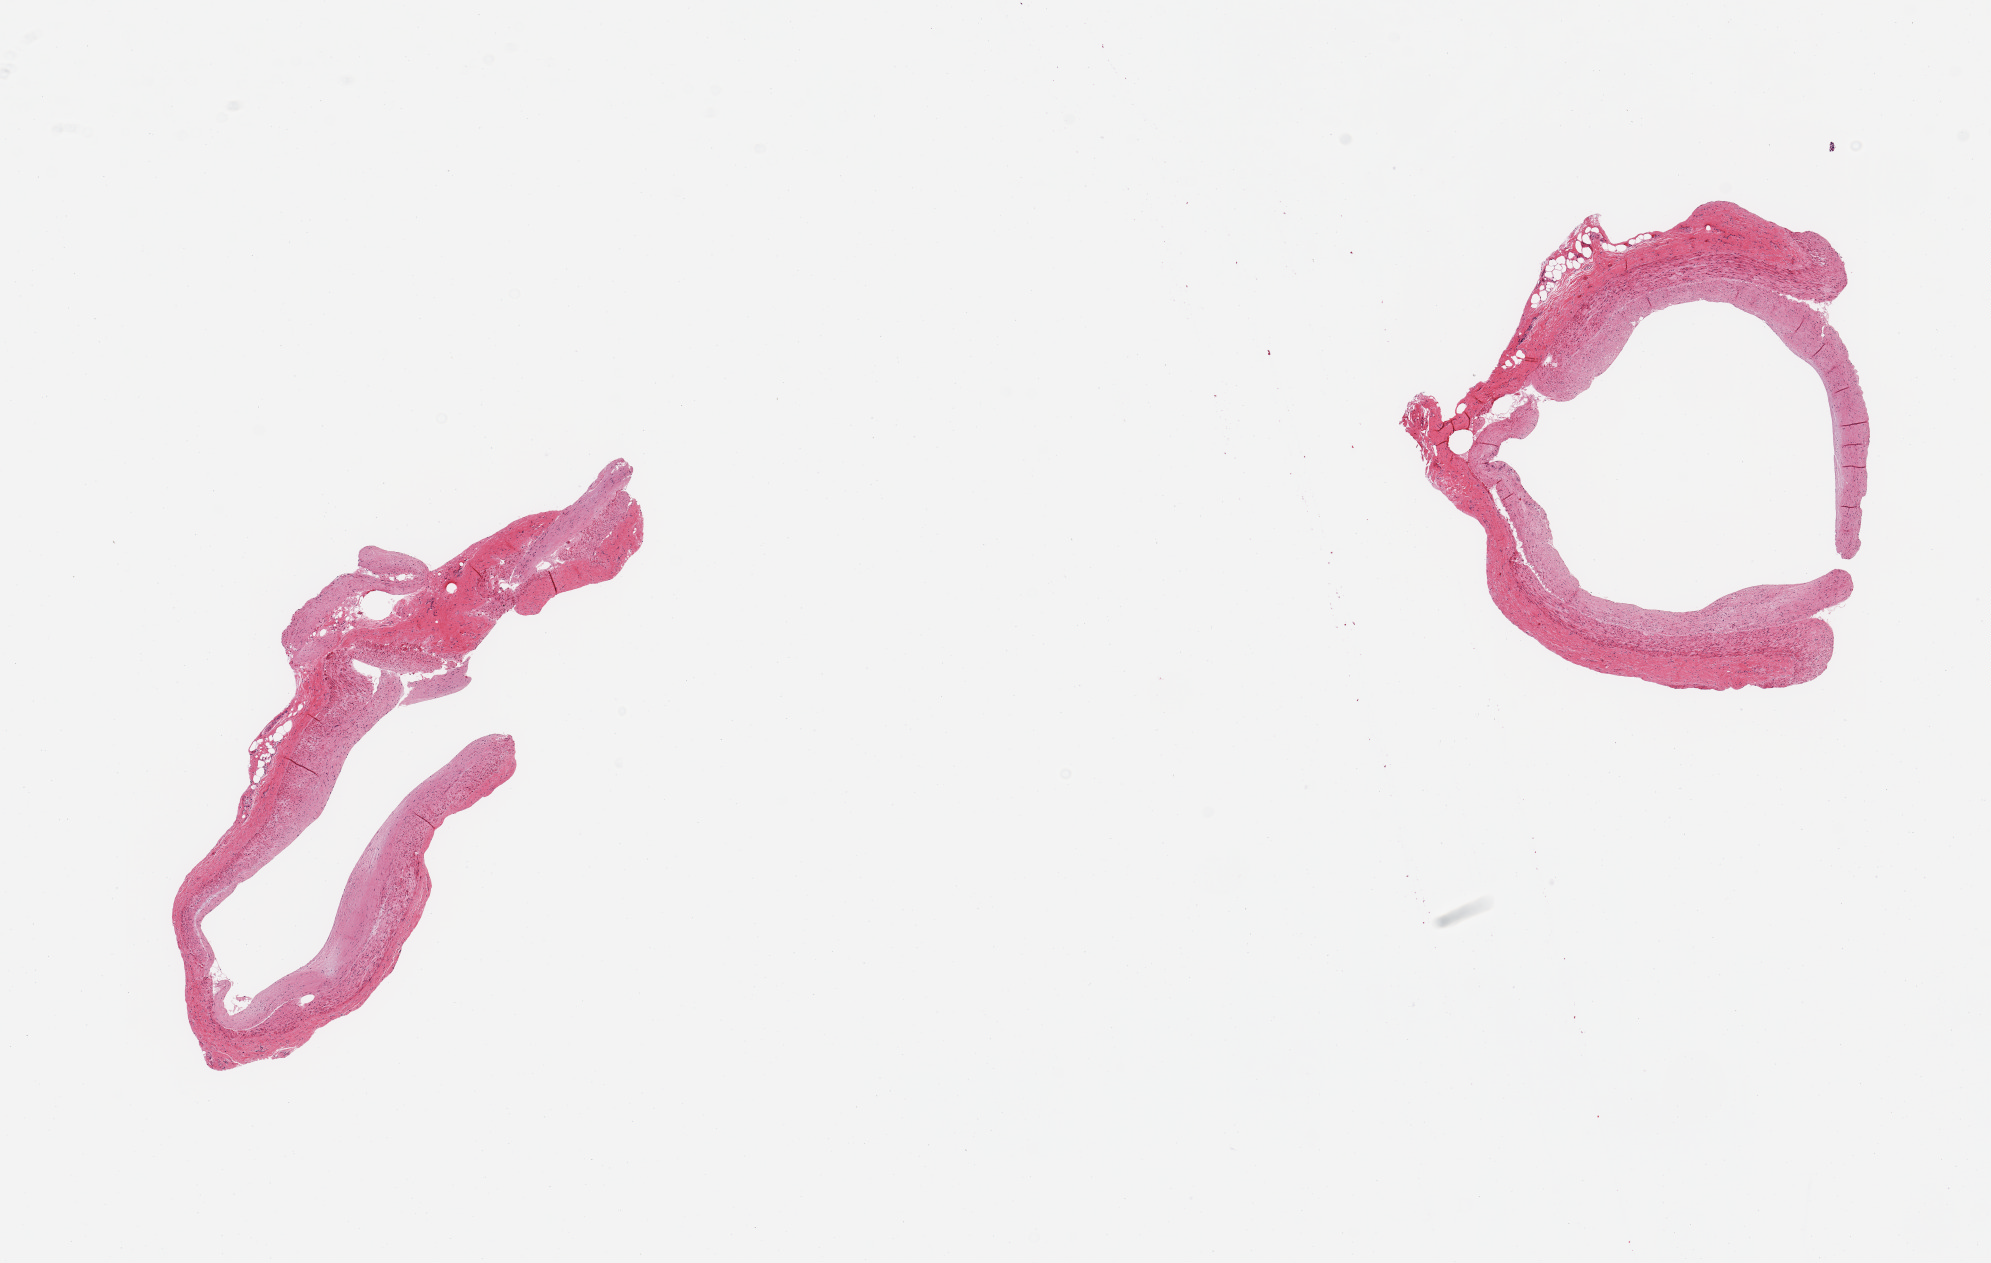
Whole-slide image, haematoxylin and eosin stain, low-resolution overview of the scanned area, about 15.8 x 10.0 mm, PAXgene-fixed paraffin-embedded (PFPE) section, sampled site (target tissue): coronary artery, tissue donor sample. Donor sex: female.
Reviewer comment on this tissue sample: 2 pieces; moderate flat atheromatous plaques.